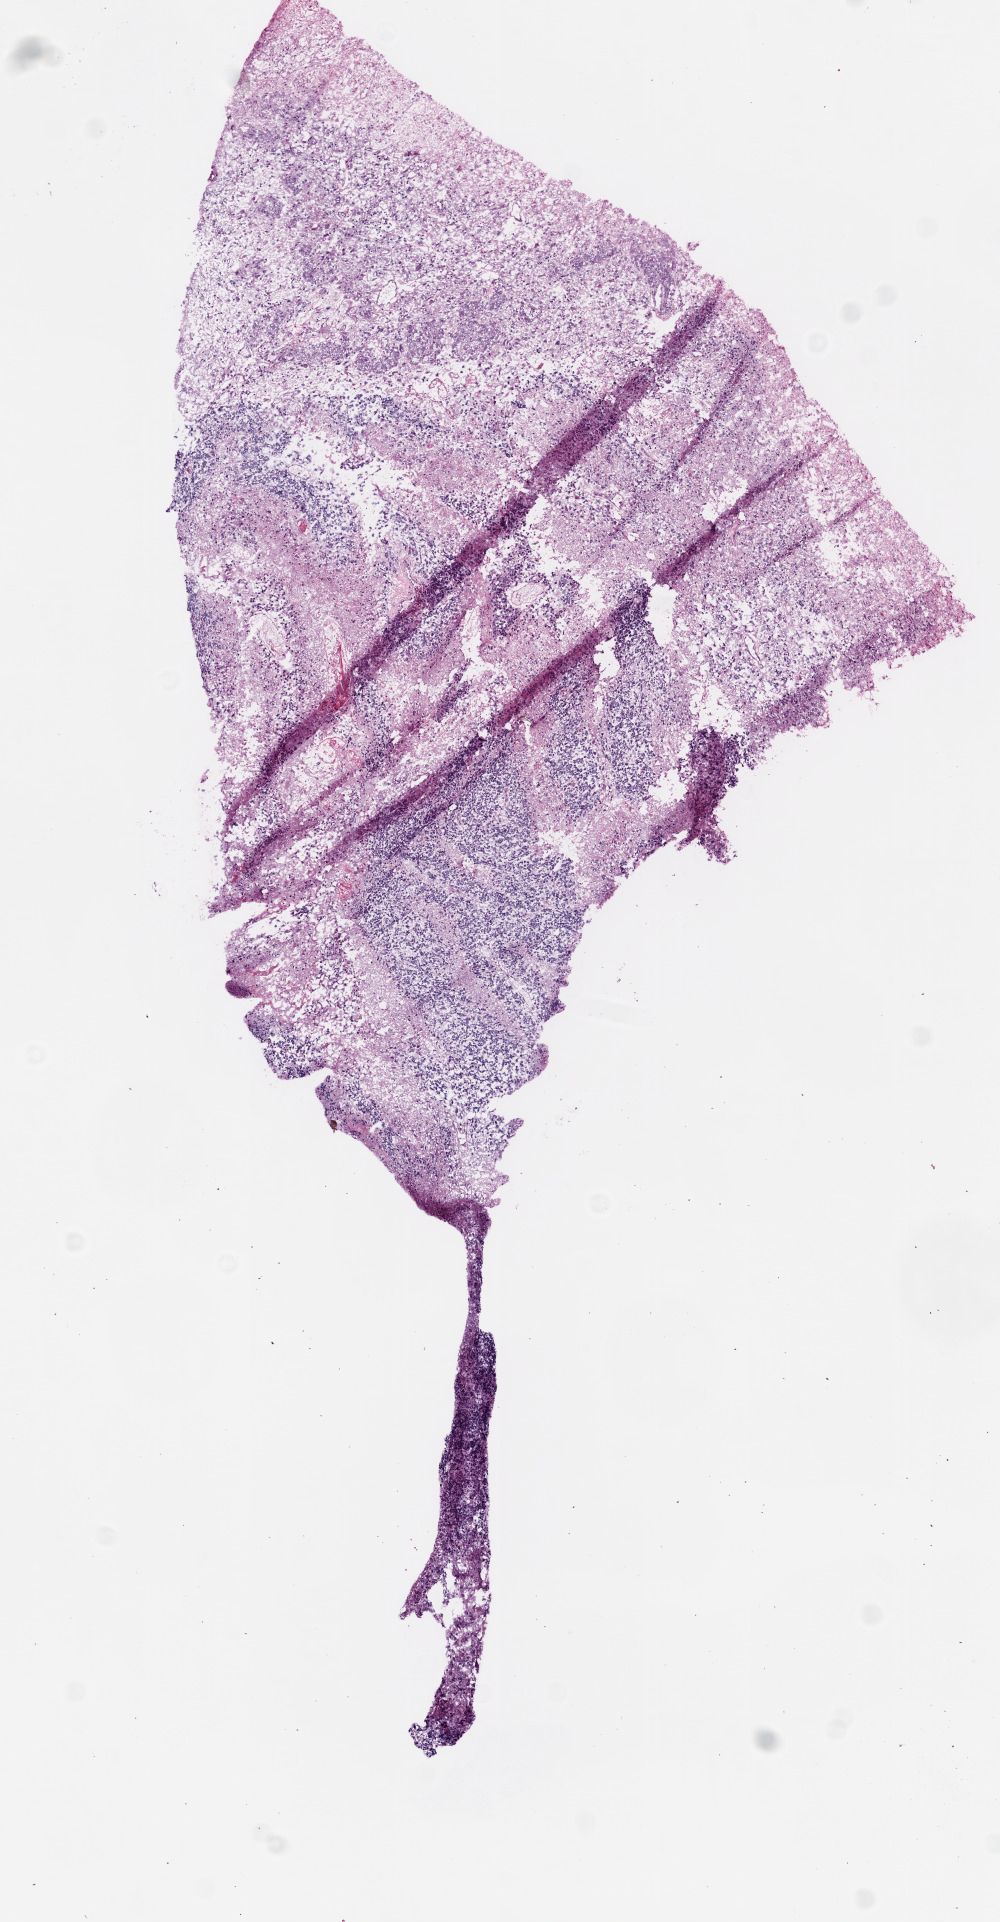
Digitized Hematoxylin and eosin (H&E) stained tissue section (whole slide) — a low-resolution overview of the entire scanned area, about 4.0 x 7.7 mm, frozen section, primary tumour sample from the brain. Male patient; age at initial diagnosis 82 years. Composition of this section per pathologist review: tumour cells 80%, tumour nuclei 85%, normal cells 0%, stromal cells 0%, necrosis 20%.
- diagnosis: Glioblastoma